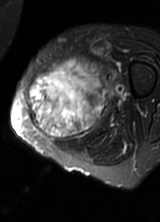
MRI of an extremity soft-tissue mass, one axial slice; slice 24 of 69 in the series (ordered by position); T2-weighted fat-saturated; MR volume resampled by the dataset authors to the PET/CT grid (not the native acquisition matrix); 3.27 mm slice thickness; 160 × 222 image matrix. Female patient. Case-level facts recorded for this patient, not image findings: histological type: pleomorphic leiomyosarcoma; grade: high; site of the primary tumour: left thigh.
Annotated regions visible in this slice (expert contour drawn on MRI and transferred to this co-registered scan by the dataset authors):
- gross tumour volume including surrounding oedema: box from (x=25, y=59) to (x=112, y=140) px
- gross tumour volume (mass): (x=25, y=68)–(x=106, y=140)